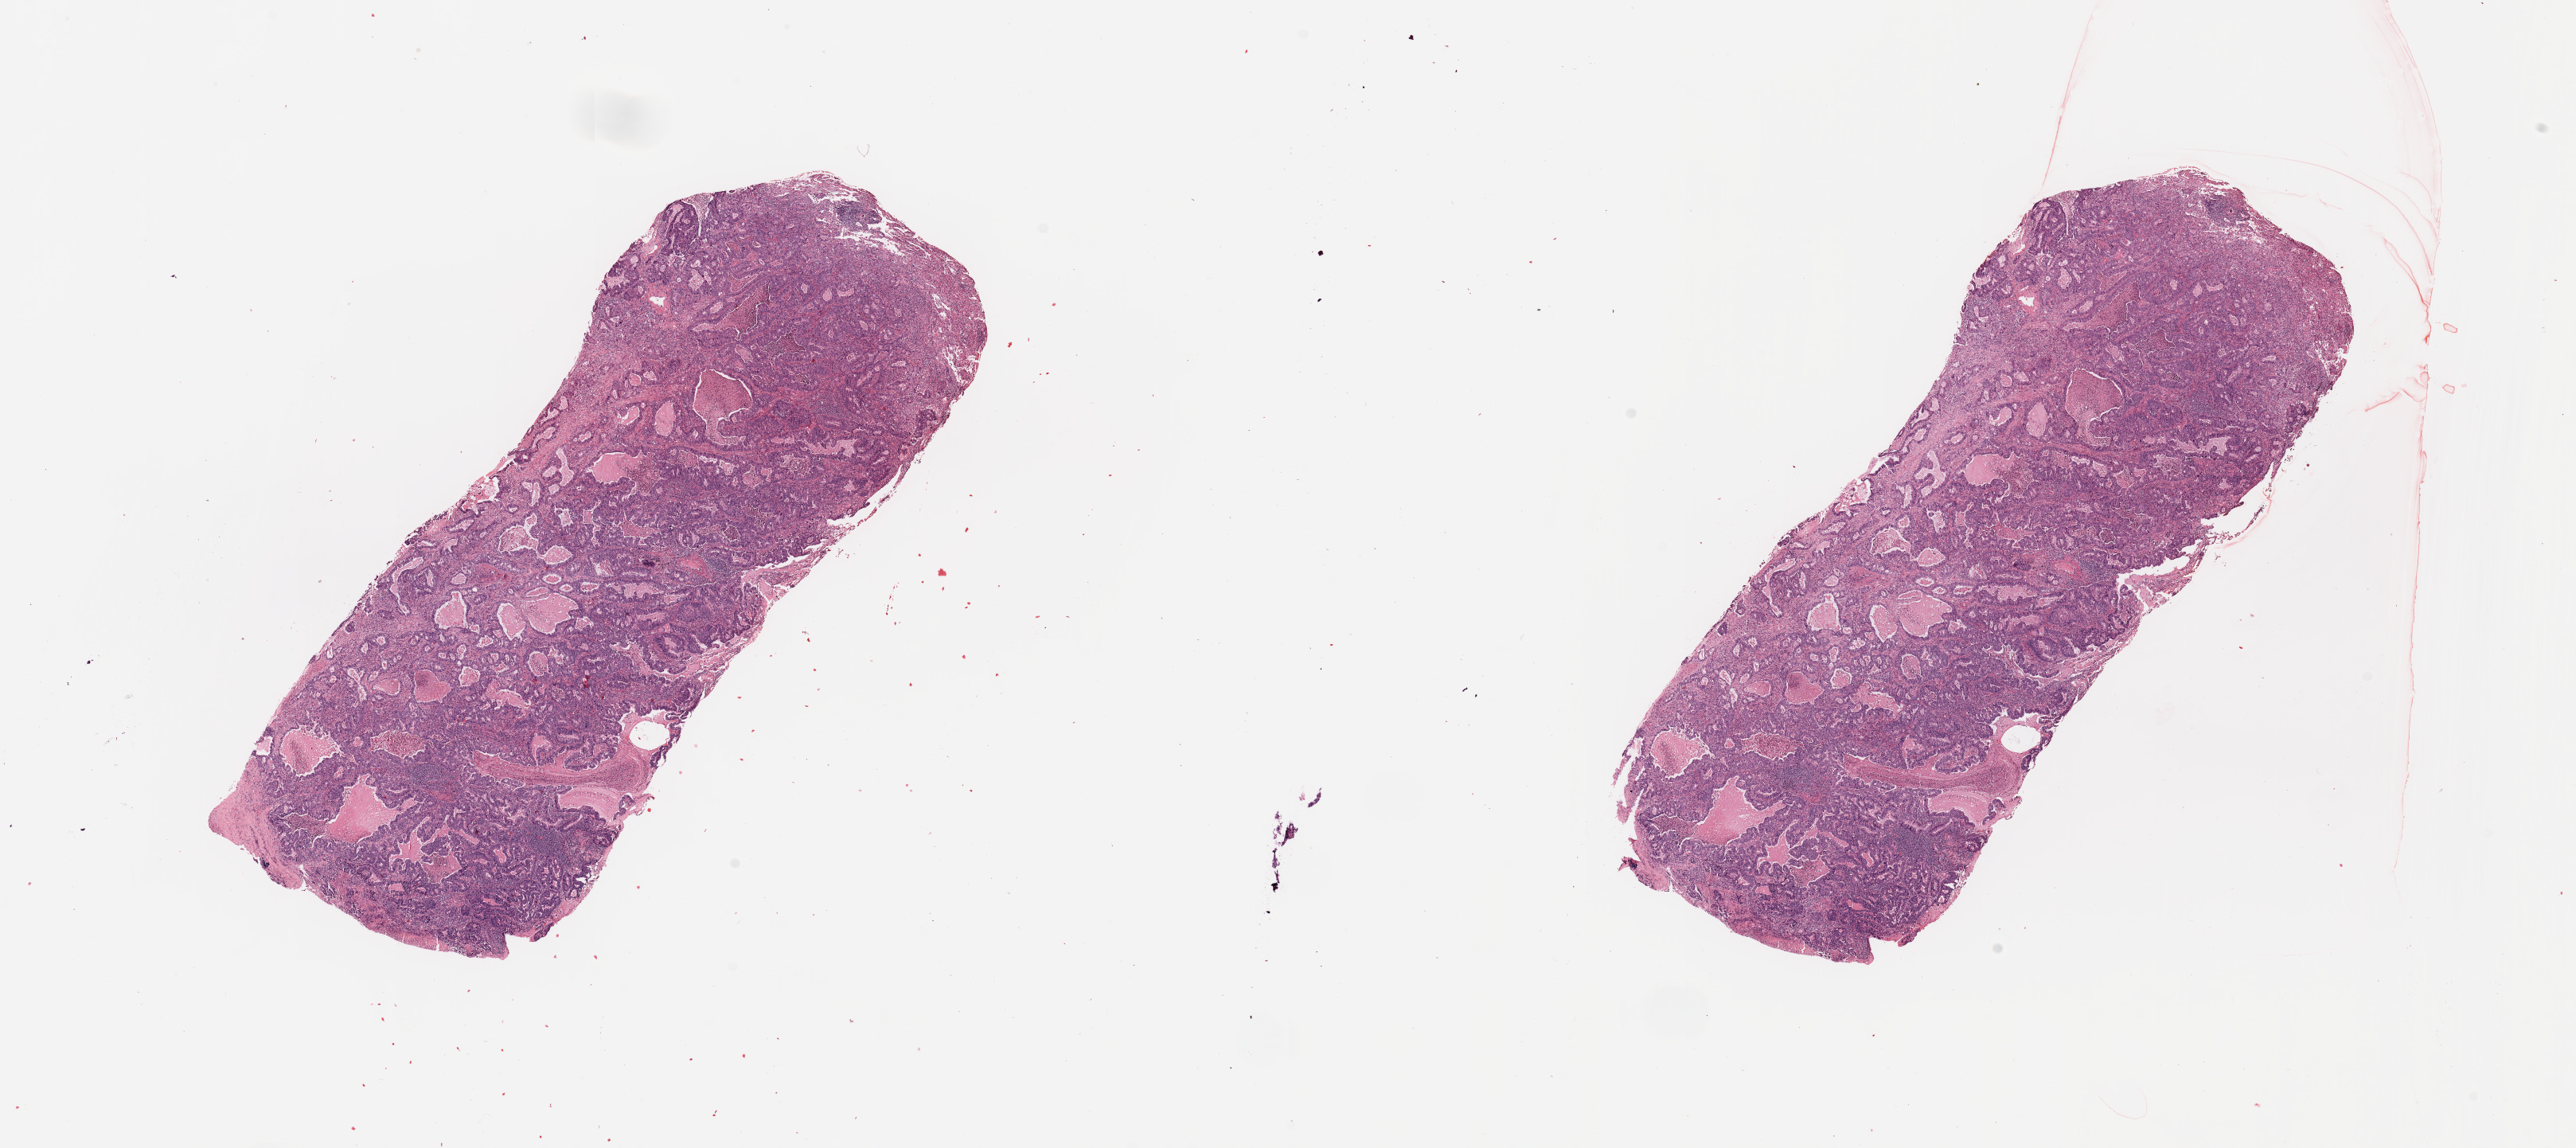
H&E-stained whole-slide image, whole scanned area (about 25.6 x 11.4 mm, acquisition: 20x scan) shown as a low-resolution overview, tumour tissue sample, lung. Male, 63 y/o. Histologic grade: G2 (moderately differentiated).
Histologic diagnosis: Adenocarcinoma, NOS. Primary tumour site (as recorded): right middle lobe. AJCC pathologic stage: IIA.